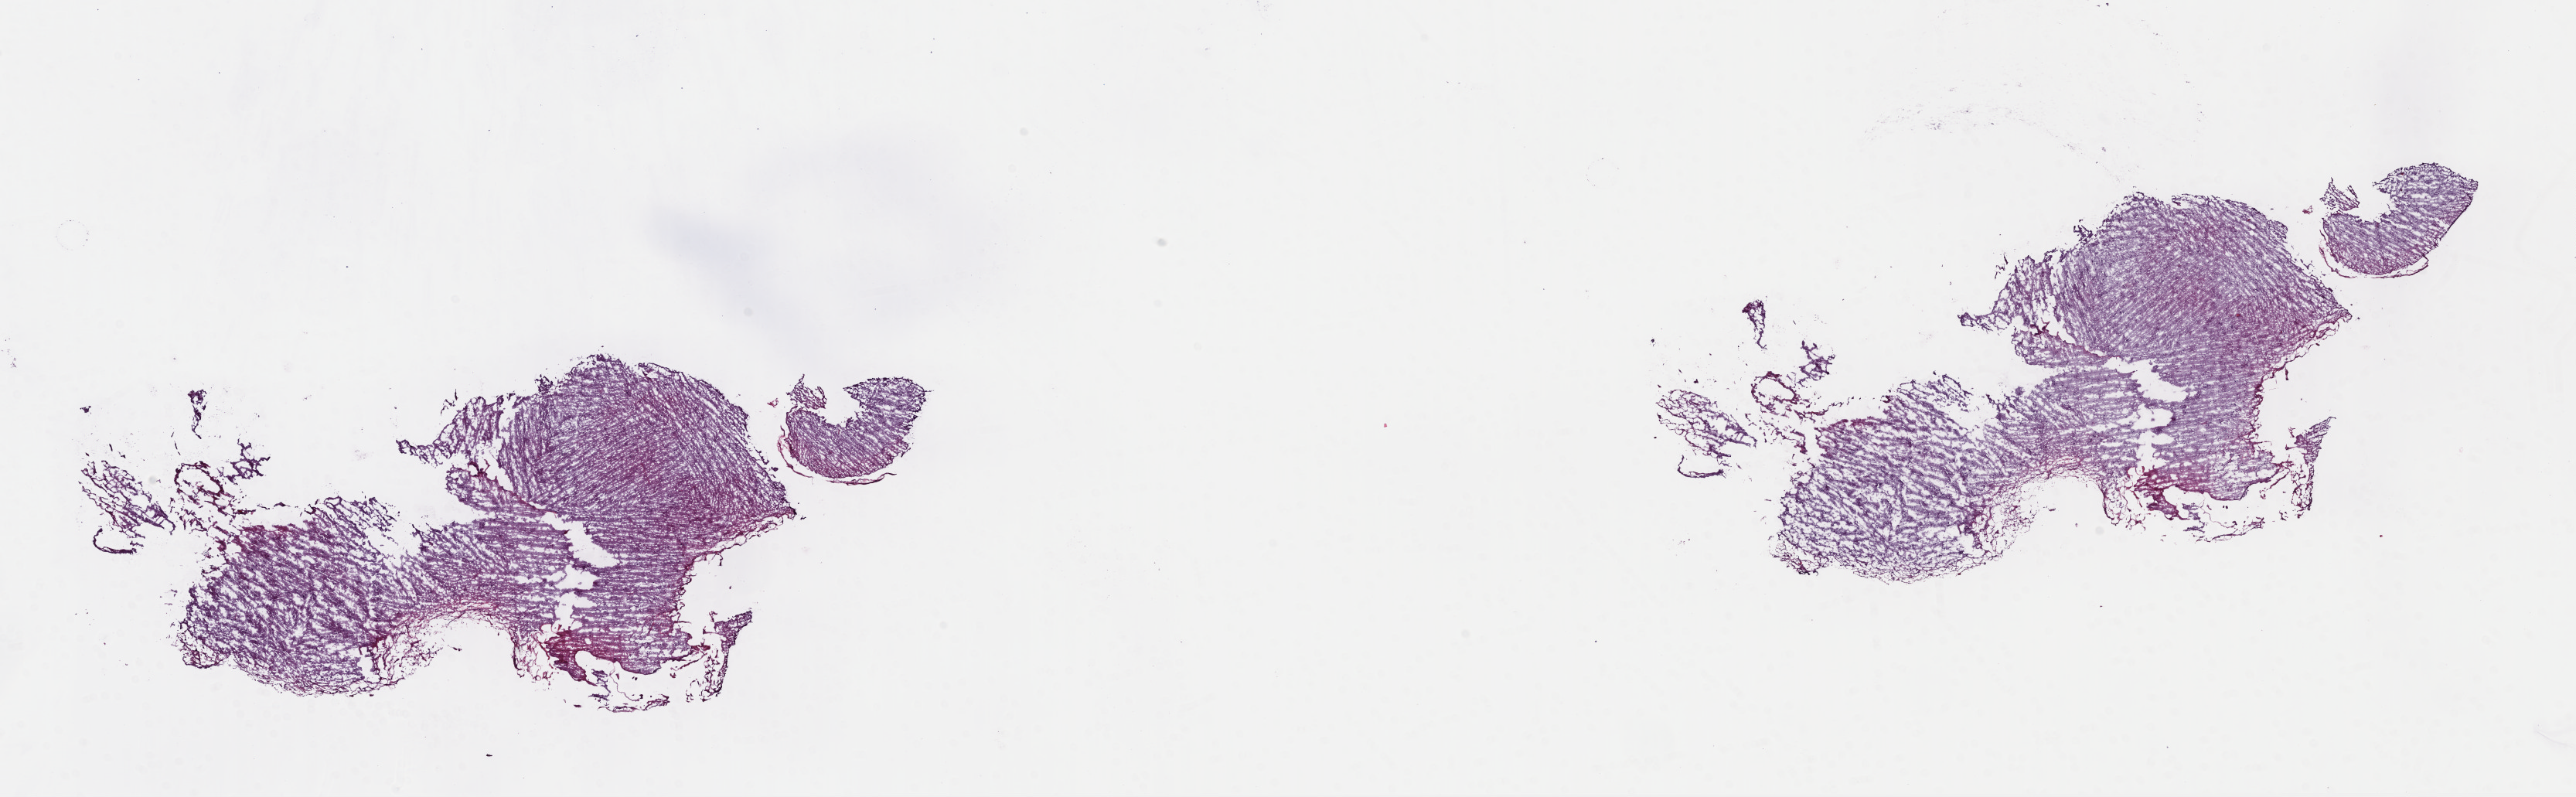
Whole-slide histology image, H&E — whole scanned area (about 26.2 x 8.1 mm, slide scanned at 40x) shown as a low-resolution overview; frozen section from the top of the tissue portion; brain, primary tumour sample. Male patient; age at initial diagnosis 21 years. Histologic grade: G2 (moderately differentiated). Slide review estimates, as recorded: tumour cells 20%, tumour nuclei 70%, normal cells 5%, stromal cells 75%, necrosis 0%. Infiltration values recorded for this section: lymphocyte infiltration 0%, monocyte infiltration 0%, neutrophil infiltration 0%.
- pathologic diagnosis: Astrocytoma, NOS (cerebrum)